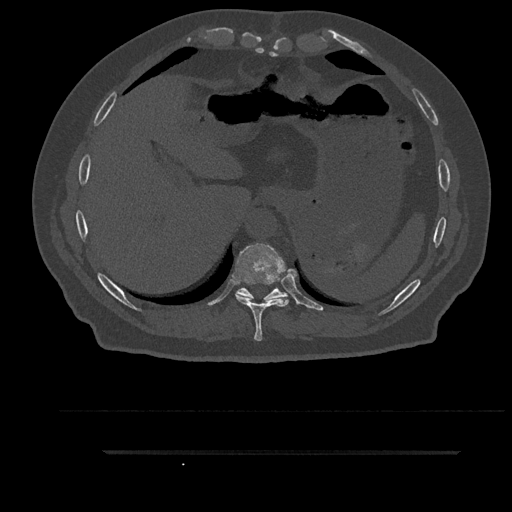
CT including the spine, one axial slice; slice 400 of 797 in the series (ordered by position); reconstruction kernel Br40s/3; 120 kVp; bone window (W 1800 / L 400 HU); 0.5 mm slice thickness; 512 × 512 image matrix. Male patient, age 63 years. From the clinical record (not read from this slice): primary cancer: renal; vertebrae with lytic lesions (as recorded): T8.
Annotated regions visible in this slice (semi-automatically segmented with operator editing):
- T10 vertebra: box from (x=235, y=288) to (x=288, y=300) px
- T9 vertebra: (x=234, y=243)–(x=289, y=341)